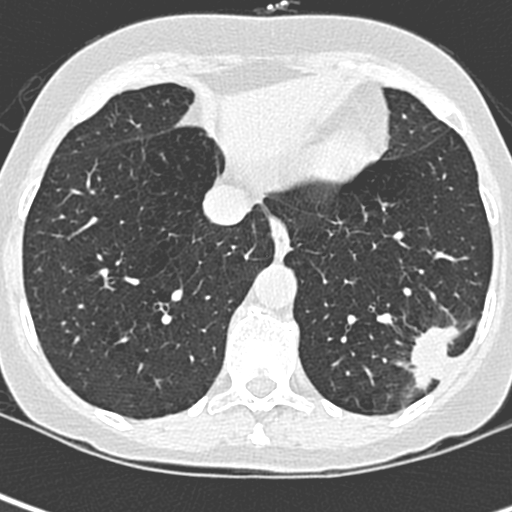
Low-dose screening chest CT, one axial slice. Position 82 of 252 along the scan axis. Lung window (W 1500 / L -600 HU). 1.3 mm slice thickness. 512 × 512 image matrix.
Annotated regions visible in this slice (expert manual segmentation):
- lesion 1 (tumor, lower lobe of left lung): bounding box <399,325,460,392> (left, top, right, bottom; pixels)